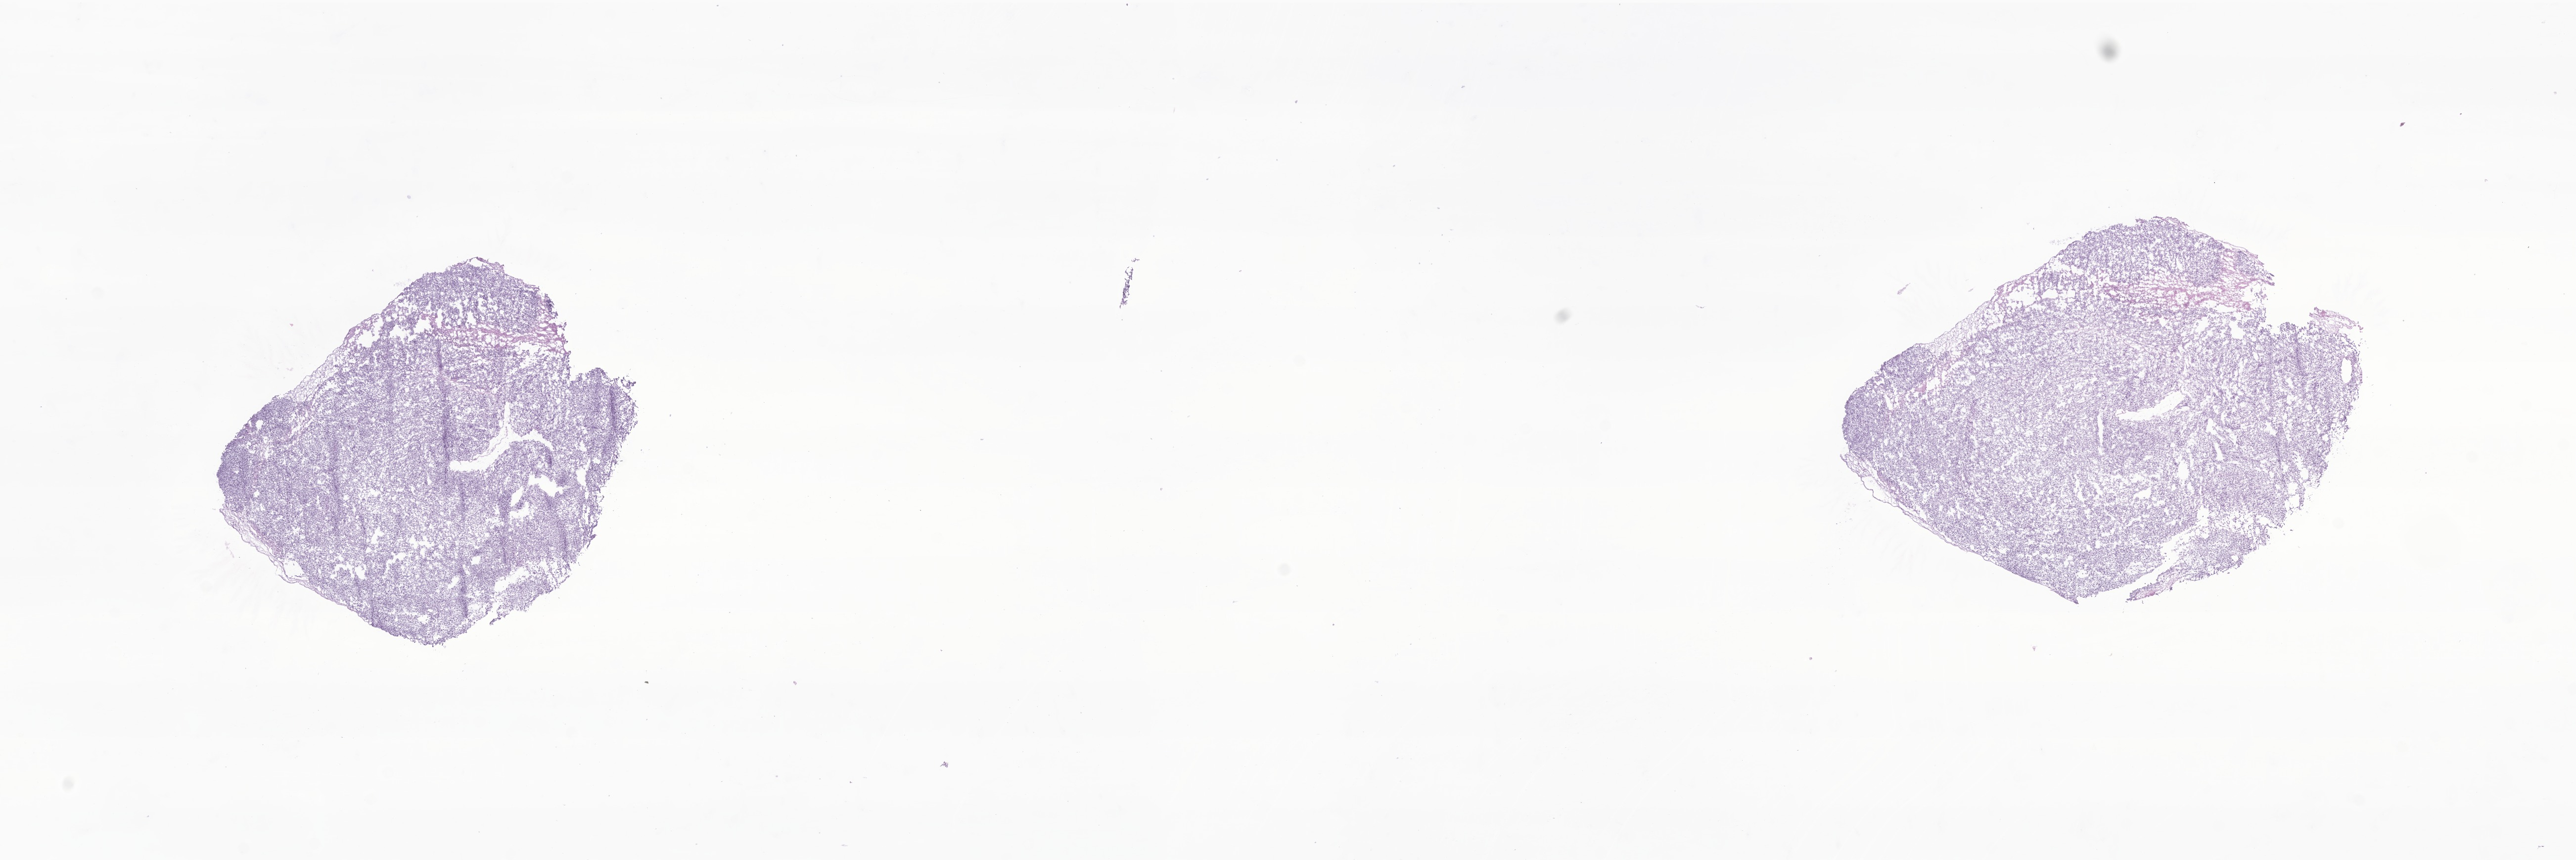
Digitized H&E-stained section of tumor tissue from the abdomen — a low-resolution overview of the entire scanned area, about 22.0 x 7.3 mm, cryosection (OCT / tissue freezing medium). Patient: male, age 44 months.
- recorded diagnosis: Undifferentiated sarcoma